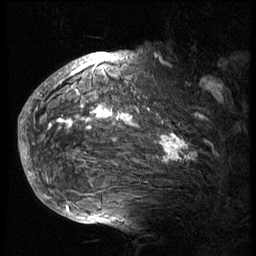
Breast MRI (dynamic contrast-enhanced), one sagittal slice; slice 54 of 74 in the series (ordered by position); 3 images stored at this slice position (order not interpretable as contrast timing); 1.5 T; TE 4.2 ms, TR 8.9 ms; 2.5 mm slice thickness; 256 × 256 image matrix, field of view 200 × 200 mm. Patient: female, 57 years. From the clinical record (not read from this slice): setting: breast cancer imaged before/during neoadjuvant chemotherapy; receptor status: HER2-positive.
Outlined on this slice (semi-automatically segmented with operator editing):
- analysis volume of interest (the breast-tissue region the enhancement analysis was run in; not a lesion): box from (x=40, y=62) to (x=234, y=175) px
- tumour enhancement mask (voxels above the 140 % enhancement threshold inside the analysis volume of interest): (x=40, y=62)–(x=198, y=163)